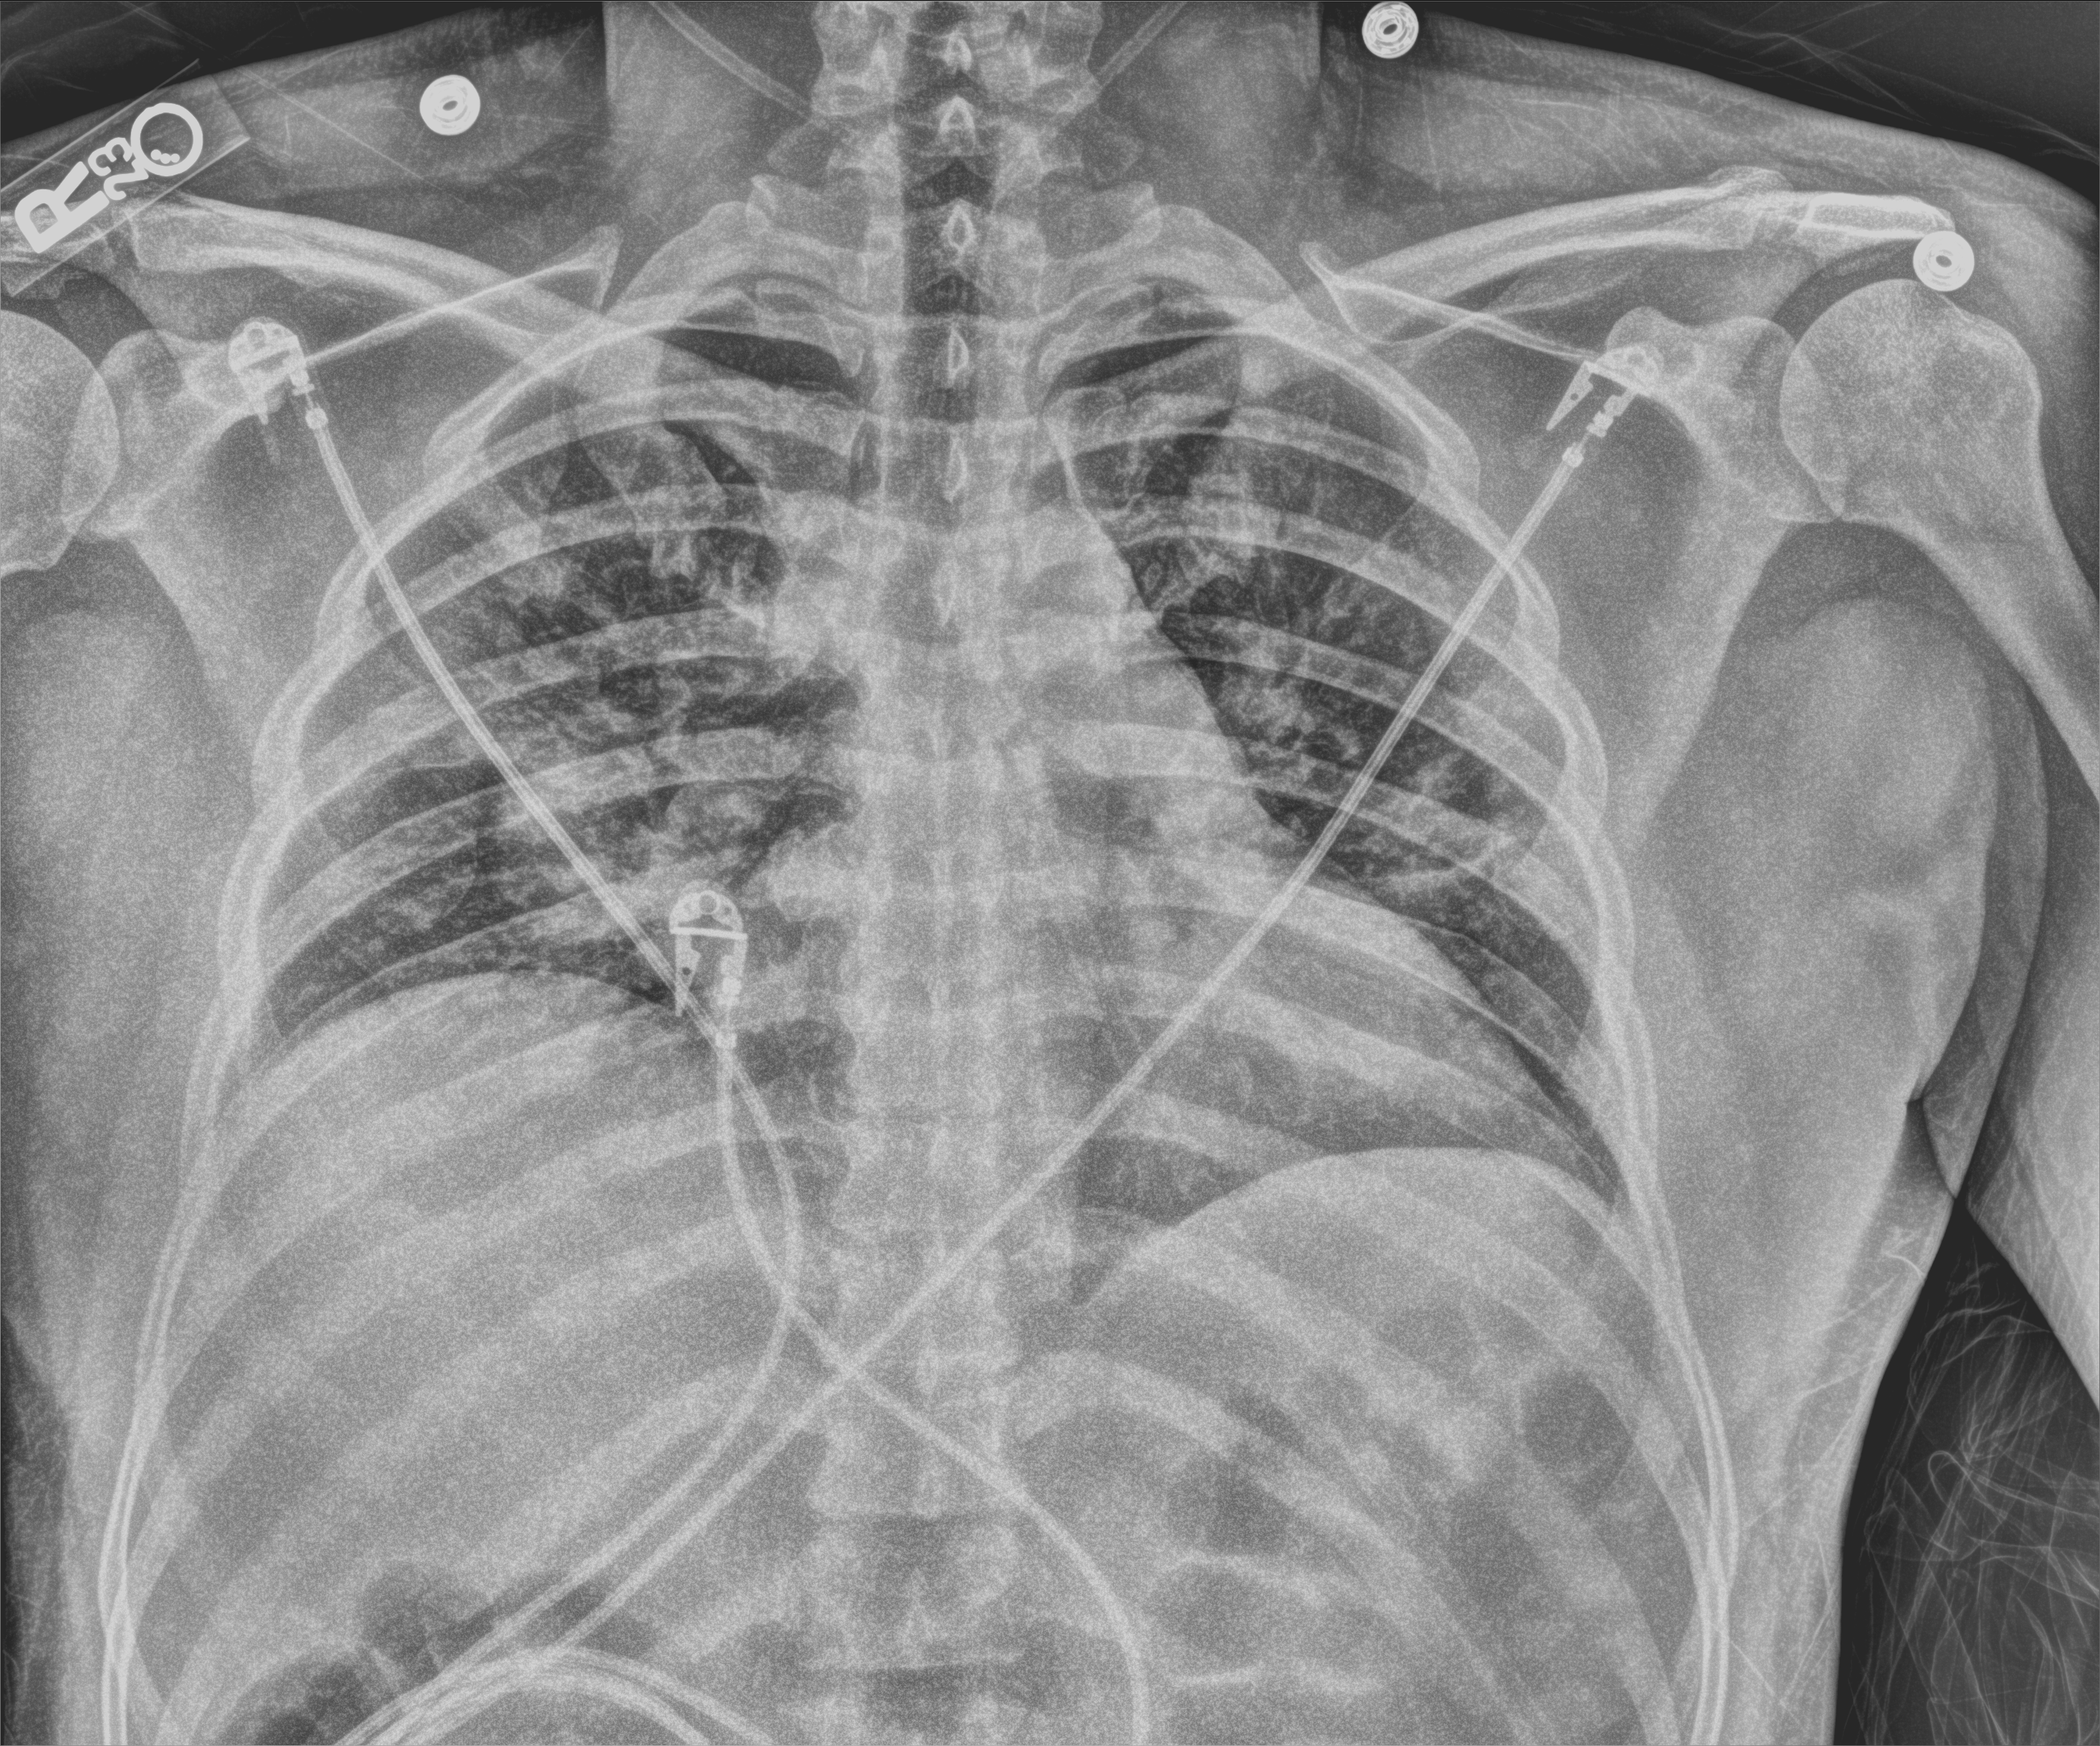
Chest X-ray (portable); anteroposterior (AP) projection. Patient hospitalised with COVID-19; male, aged 18–59 years.
From the hospital-stay record, not from the radiograph (when in the stay this image was taken is not recorded): admitted to intensive care during this hospital stay: no; mechanically ventilated during this hospital stay: no; hypertension (admission record): yes.